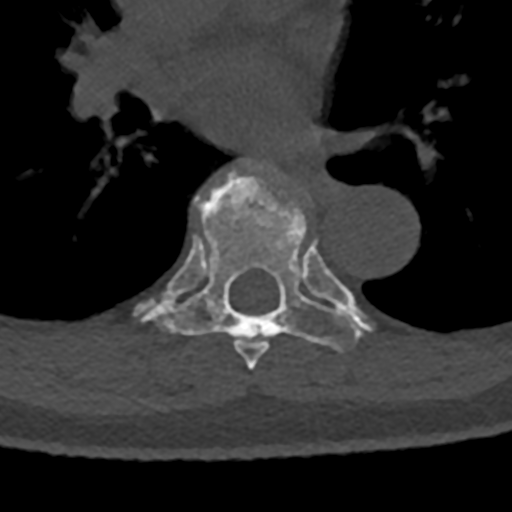
CT including the spine, one axial slice; slice 774 of 797 in the series (ordered by position); reconstruction kernel Br40s/3; bone window (W 1800 / L 400 HU); 512 × 512 image matrix, field of view 160 × 160 mm. Patient: male, 74 years. From the clinical record (not read from this slice): primary cancer: renal.
Structures marked on this image (semi-automatic segmentation, software-assisted and operator-edited):
- T6 vertebra: box from (x=235, y=341) to (x=269, y=370) px
- T7 vertebra: (x=134, y=168)–(x=372, y=350)